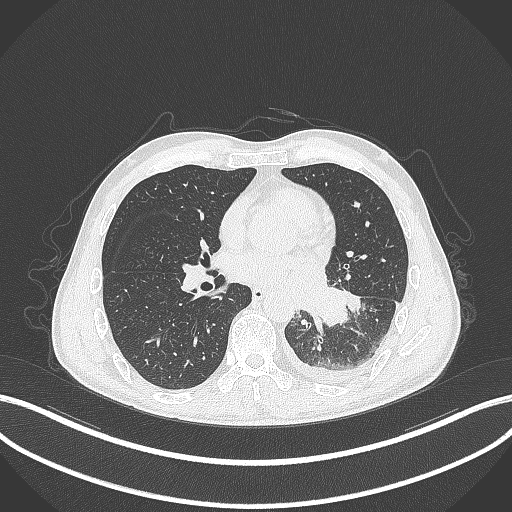
Chest CT, one axial slice. Slice 143 of 295 in the series (ordered by position). Reconstruction kernel B70f. Lung window (W 1500 / L -600 HU). 512 × 512 image matrix, field of view 400 × 400 mm. Male patient, age 47 years. From the clinical record (not read from this slice): clinical TNM (as recorded): T3 N1 M1c; histopathological grade: G3.
Structures marked on this image (bounding box drawn by a radiologist):
- lung tumour (recorded histology: small cell carcinoma): bounding box <308,285,349,334> (left, top, right, bottom; pixels)